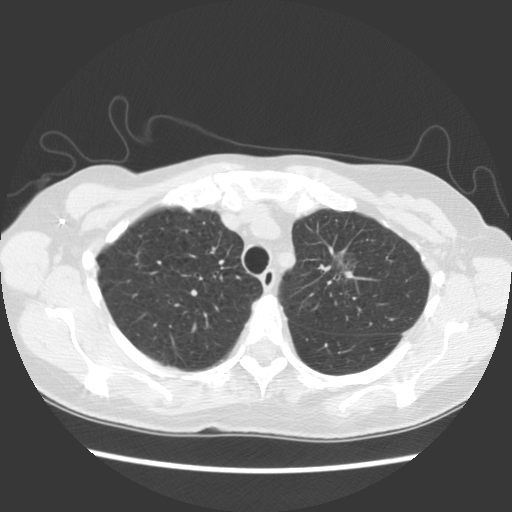
Chest CT (low-dose screening protocol), one axial image; baseline screening round; lung window (W 1500 / L -600 HU); 2.5 mm slice thickness; 140 kVp; 512 × 512 image matrix, field of view 325 × 325 mm. Female participant, aged 65 years at enrolment.
Lesion marked by an expert reader, bounding box [x1, y1, x2, y2] px = [312, 235, 379, 296]. Screening reader's record for this exam (one nodule recorded; not confirmed to be the boxed lesion): non-calcified nodule or mass ≥4 mm, left upper lobe, 11 × 10 mm, poorly defined margins, ground glass attenuation. Official screen result: positive, change unspecified: nodule(s) >= 4 mm or enlarging nodule(s), mass(es), or other non-specific abnormalities suspicious for lung cancer. Participant outcome: lung cancer diagnosed 810 days after this screen — adenocarcinoma, NOS, left upper lobe, moderately differentiated (G2), stage IA (AJCC 6th edition), 30 mm at pathology.